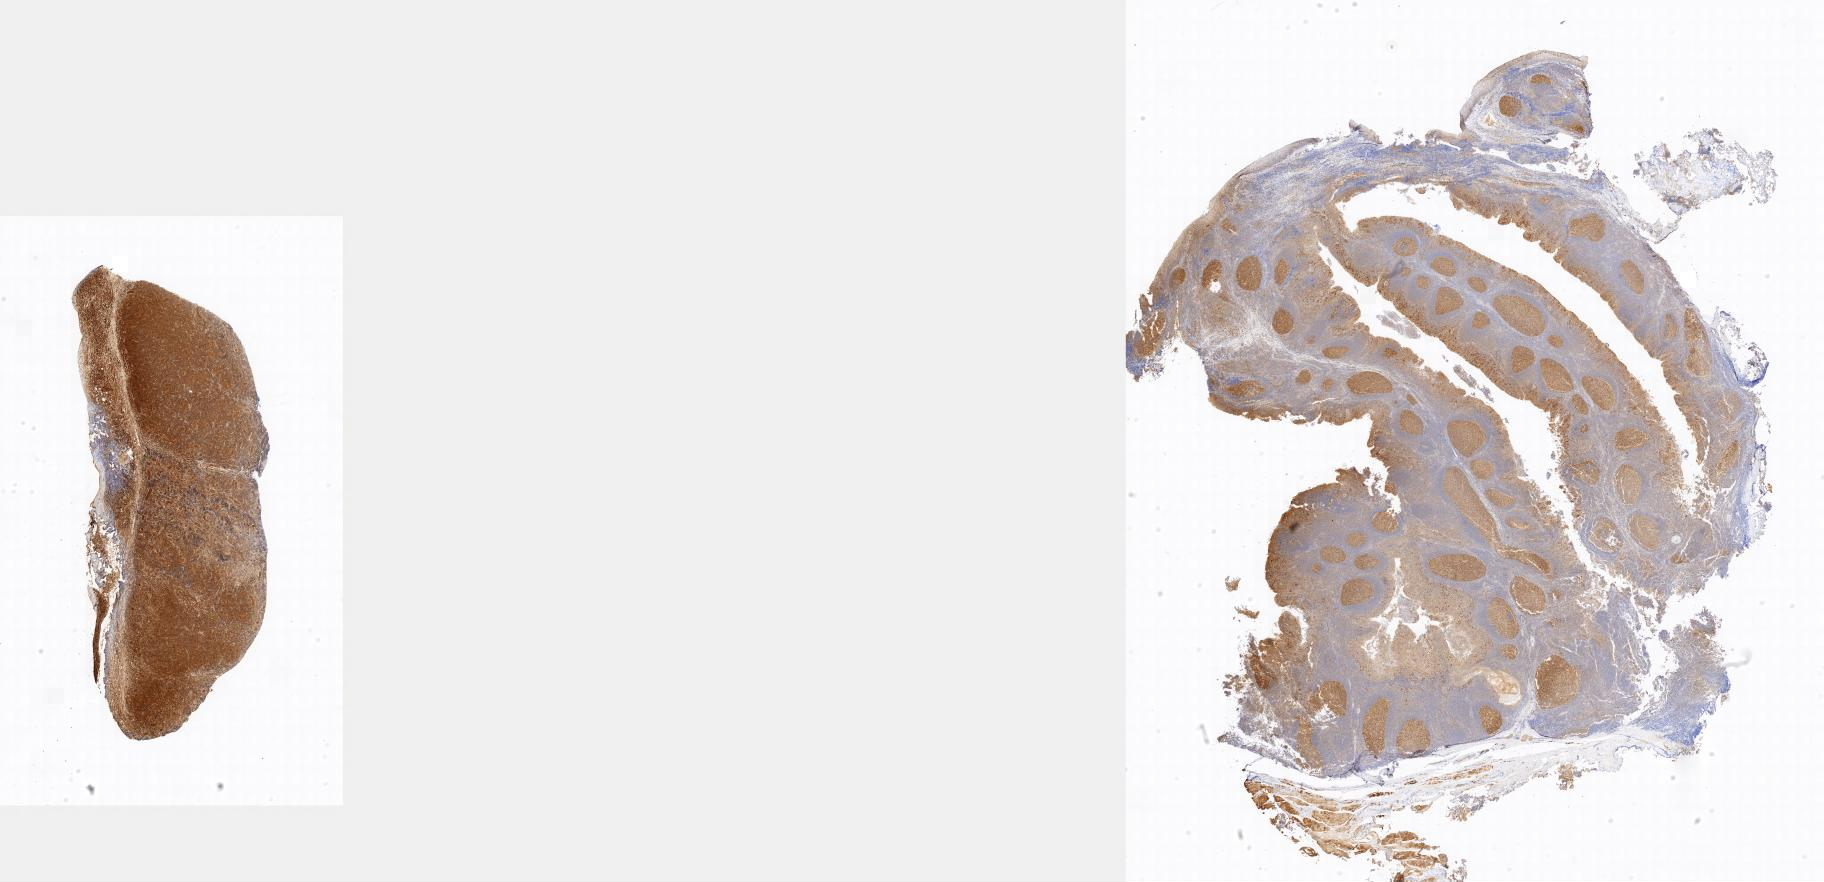
Immunohistochemistry (IHC) whole-slide image stained for BCL6 — low-resolution overview of the scanned area, specimen: tumor tissue, site: testis. Male patient; age at initial diagnosis 8 years.
* diagnosis: Burkitt lymphoma, NOS